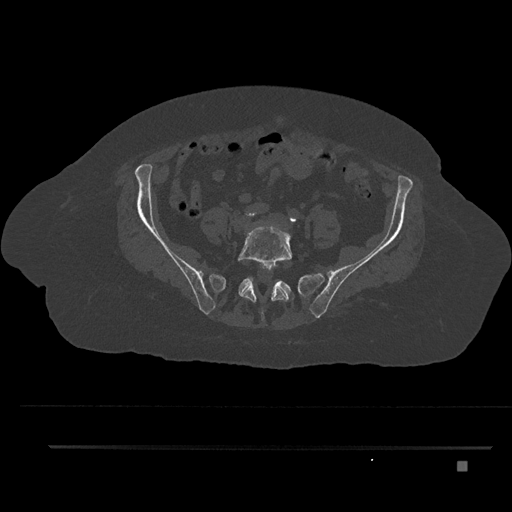
CT including the spine, one axial slice; slice 30 of 797 in the series (ordered by position); reconstruction kernel Br40s/3; 120 kVp; bone window (W 1800 / L 400 HU); 0.5 mm slice thickness; 512 × 512 image matrix, field of view 437 × 437 mm. Female patient, age 76 years. From the clinical record (not read from this slice): primary cancer: lung.
Structures marked on this image (semi-automatically segmented with operator editing):
- L5 vertebra: bounding box <237,224,293,321> (left, top, right, bottom; pixels)